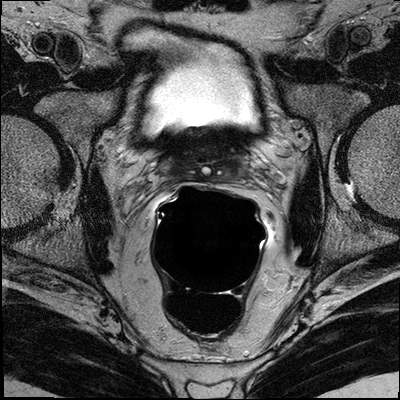
MRI of the prostate; 3 images, each a single mid-volume slice chosen by position (not for content).
Image 1: axial T2-weighted image, series "T2W_TSE_AX", slice 17 of 32.
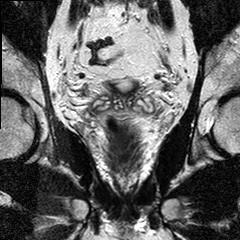
Image 2: coronal T2-weighted image, series "T2W_TSE_COR", slice 13 of 24, 3 mm slice thickness.
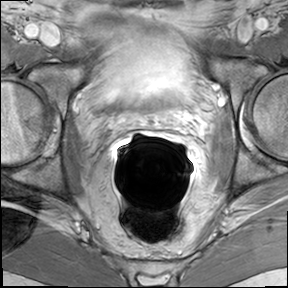
Image 3: DCE (dynamic gadolinium-enhanced) axial slice, slice 17 of 32, dynamic phase 5 of 8, 6 mm slice thickness.
MRI report (verbatim):
FINDINGS: The zonal anatomy is preserved. In the left lateral and posterio-lateral peripheral zone from 2-6 o'clock and the adjacent central gland of the prostate base, mid third, and extending into the apical third, there is a large geographic T2 hypointense area seen, with highly suspicious kinetics on the DCE series. Maximal extension of the dominant mass is 2.5 x 1.8 x 2.4 cm; There are also suspicious areas seen in the paramedian right peripheral zone and also the posterior lateral peripheral zone. 6-8 o'clock). At the mid third level the prostate left posterior lateral capsule is interrupted at 5 o'clock; in the apex between 4 and 5 o'clock the gland border is irregular or indistinct; In addition, there is suspicious enhancement seen beyond the prostate capsule in the mid-third of the prostate between 3 o'clock and 5 o'clock which is suggestive for beginning extracapsular disease (towards the left neurovascular bundle). The right neurovascular bundle is uninvolved. The seminal vesicles are unremarkable. No suspicious the enlarged obturator and iliac lymph nodes on either side. IMPRESSION: Left sided prostate tumor within the left lateral and posterior lateral peripheral zone with peripheral to the right paramedian peripheral zone; with beginning/minimal extracapsular extension left posterior-lateral towards the left neurovascular bundle; No involvement of the right neurovascular bundle; no seminal vesicles infiltration; no pelvic lymphadenopathy.